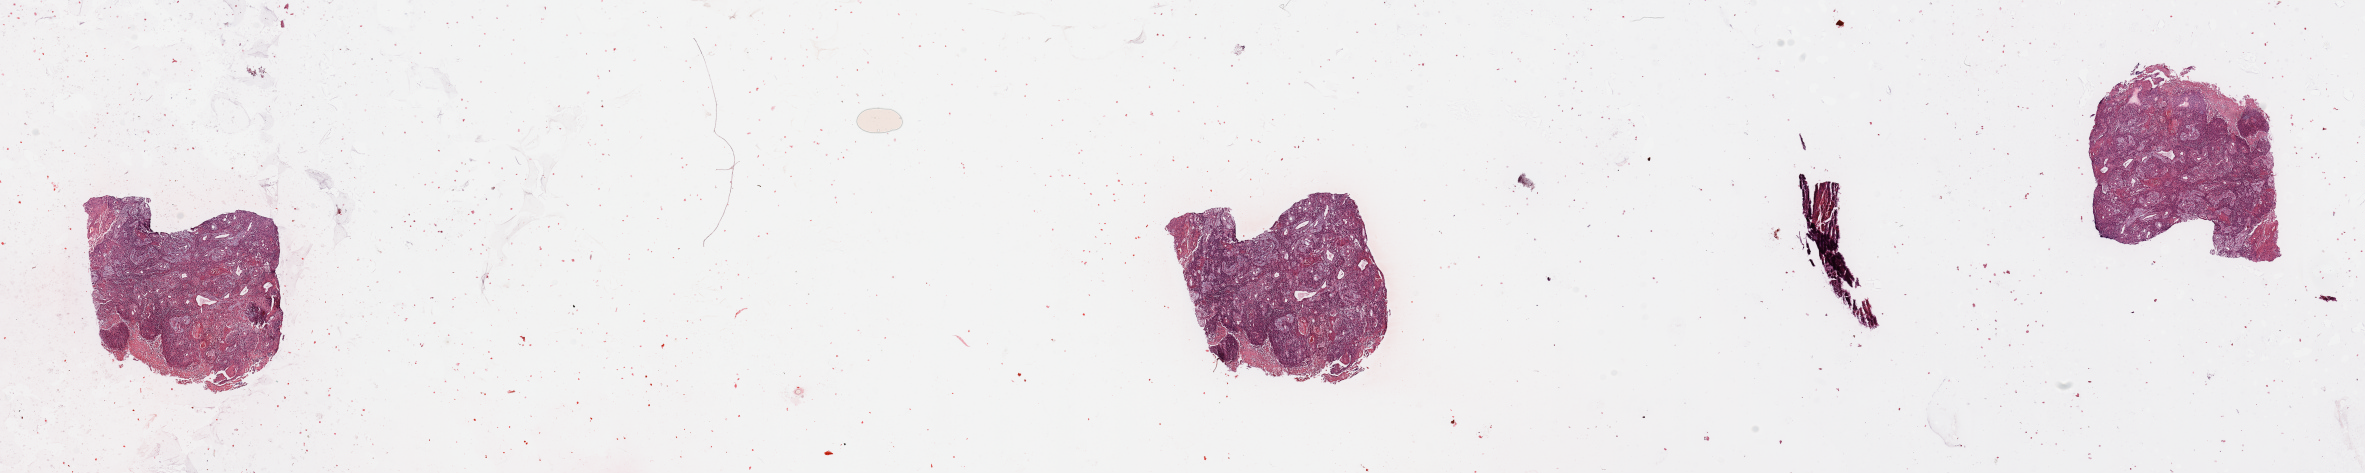
Digitized H&E tissue section (whole slide) — whole scanned area (about 37.4 x 7.5 mm, slide scanned at 20x) shown as a low-resolution overview. Tumour tissue sample, sampled site: larynx. Patient: male, age 64 years. Histologic grade: G2 (moderately differentiated). Composition of this section per pathologist review: tumour nuclei 85%, necrosis 10%.
AJCC pathologic stage: IVA. Diagnosis: Squamous cell carcinoma, NOS.